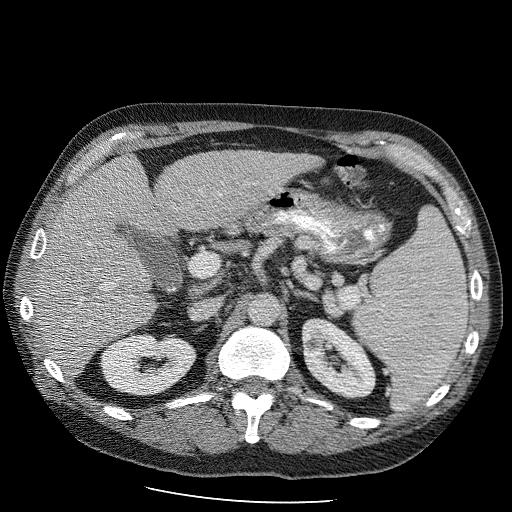
Contrast-enhanced abdominal CT (liver protocol), one axial slice. Slice 51 of 98 in the series (ordered by position). Reconstruction kernel STANDARD. Soft-tissue window (W 400 / L 40 HU). 2.5 mm slice thickness. 512 × 512 image matrix. From the clinical record (not read from this slice): diagnosis: hepatocellular carcinoma (patient treated with transarterial chemoembolisation; whether this scan precedes or follows treatment is not stated here); TNM stage (as recorded): Stage-II; Child-Pugh class: B; tumour differentiation: moderately differentiated; tumour nodularity: uninodular.
Structures marked on this image (semi-automatically segmented with operator editing):
- liver parenchyma outside the tumour (the mass and vessels are separate outlines, so this box may not span the whole liver): box from (x=28, y=148) to (x=325, y=376) px
- liver vessels: (x=40, y=242)–(x=118, y=288)